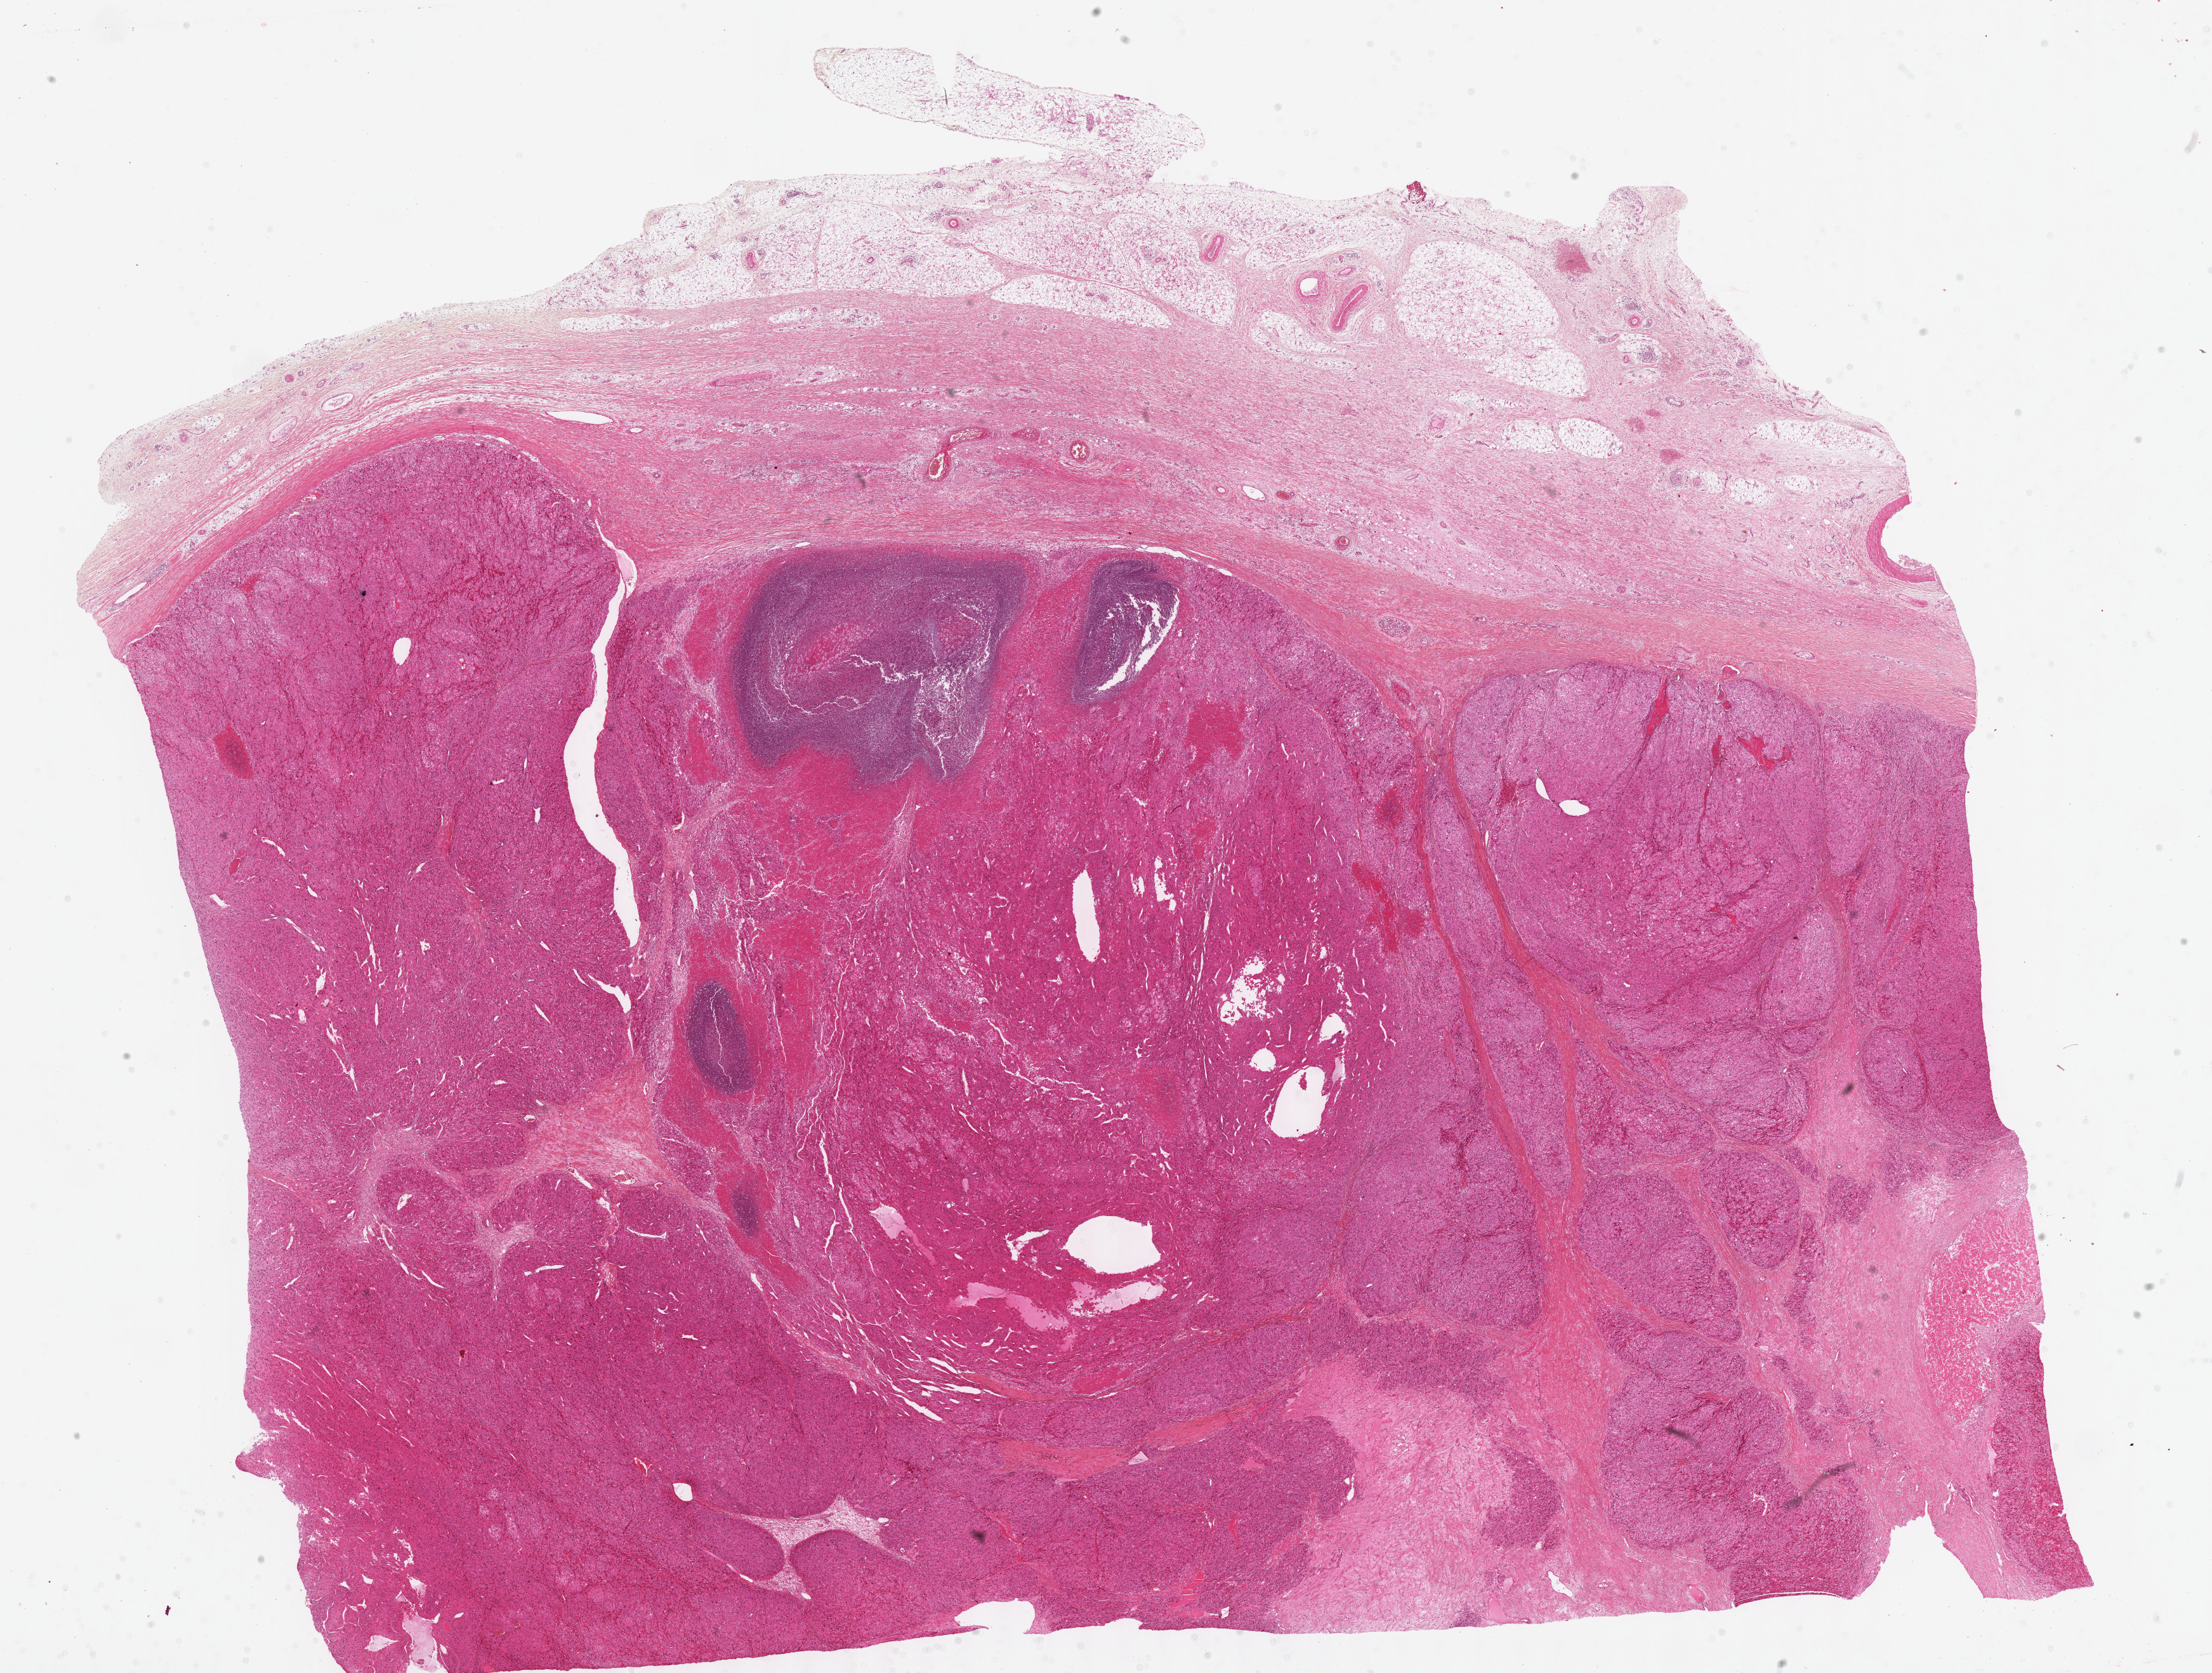
Digitized Hematoxylin and eosin (H&E) stained tissue section (whole slide), low-resolution overview of the scanned area, about 28.2 x 21.3 mm (from a 40x scan). FFPE section. Sample: primary tumour, adrenal cortex. Male patient; age at initial diagnosis 23 years.
• laterality: right
• lymph nodes positive (case pathology): 0 of 32 examined
• pathologic diagnosis: Adrenal cortical carcinoma (cortex of adrenal gland)